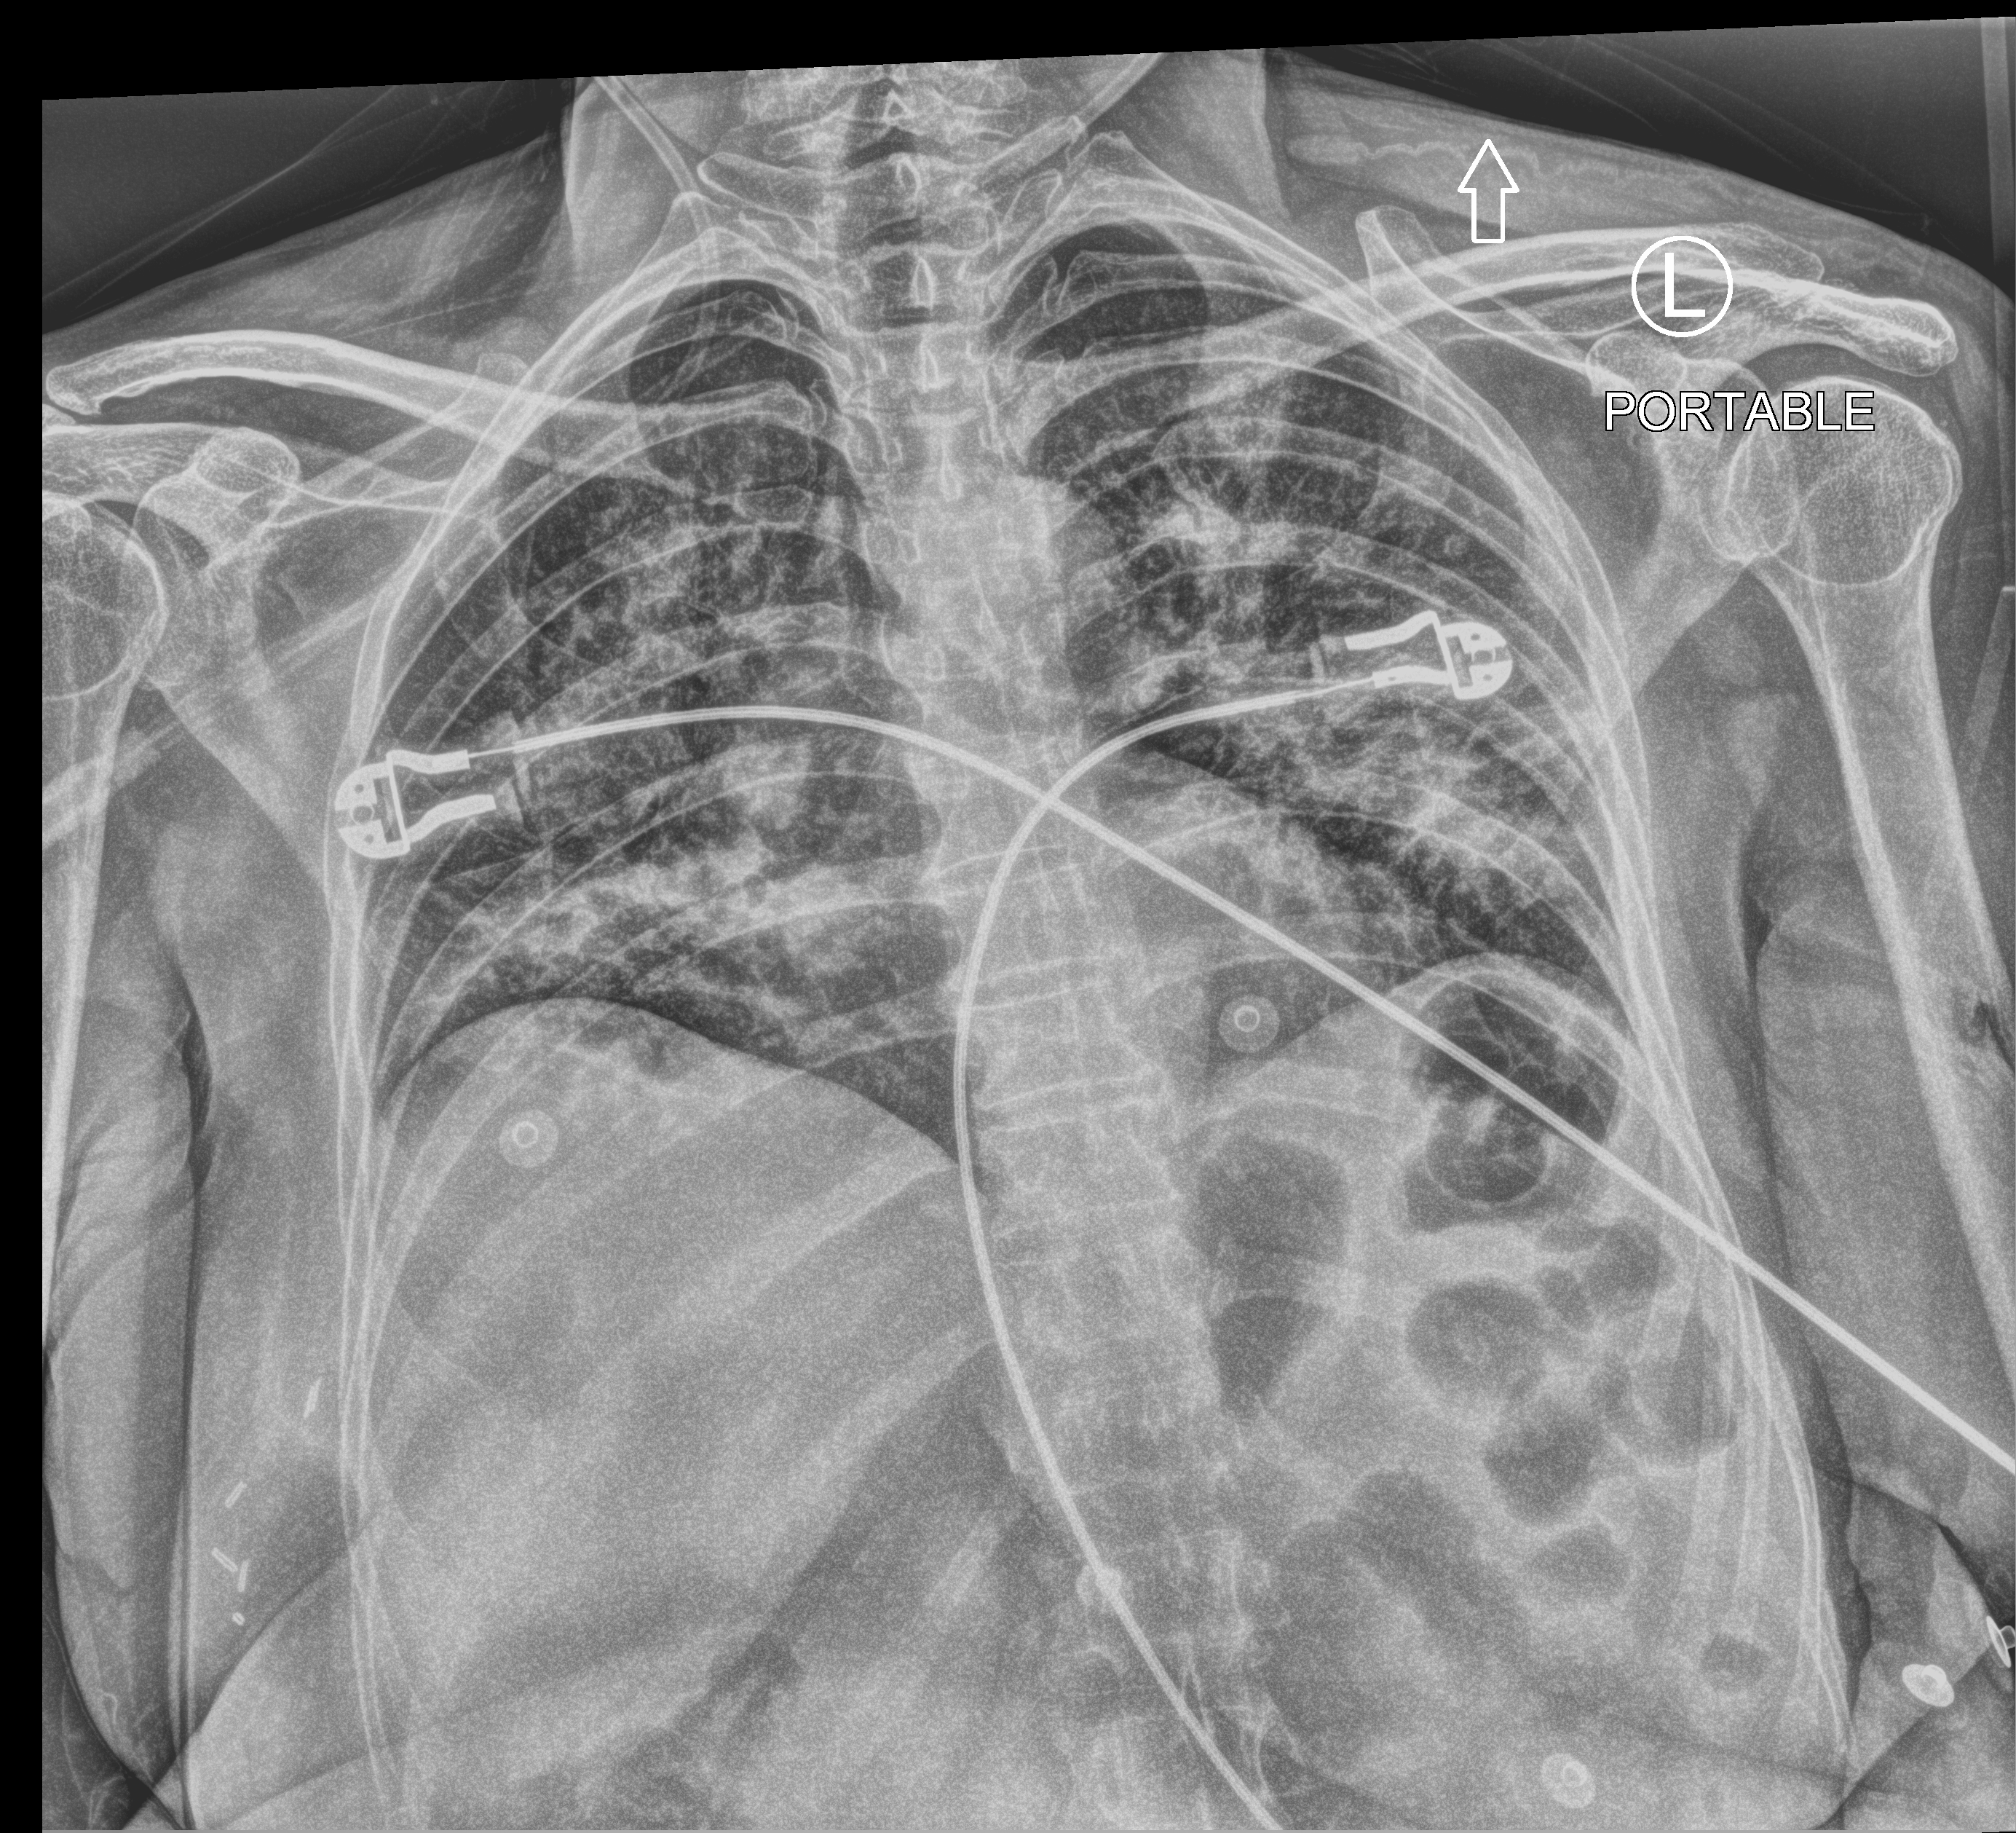
Bedside chest radiograph (computed radiography); anteroposterior (AP) projection. Female patient hospitalised with COVID-19, age 60–74 years.
From the hospital-stay record, not from the radiograph (when in the stay this image was taken is not recorded):
- admitted to intensive care during this hospital stay: no
- mechanically ventilated during this hospital stay: no